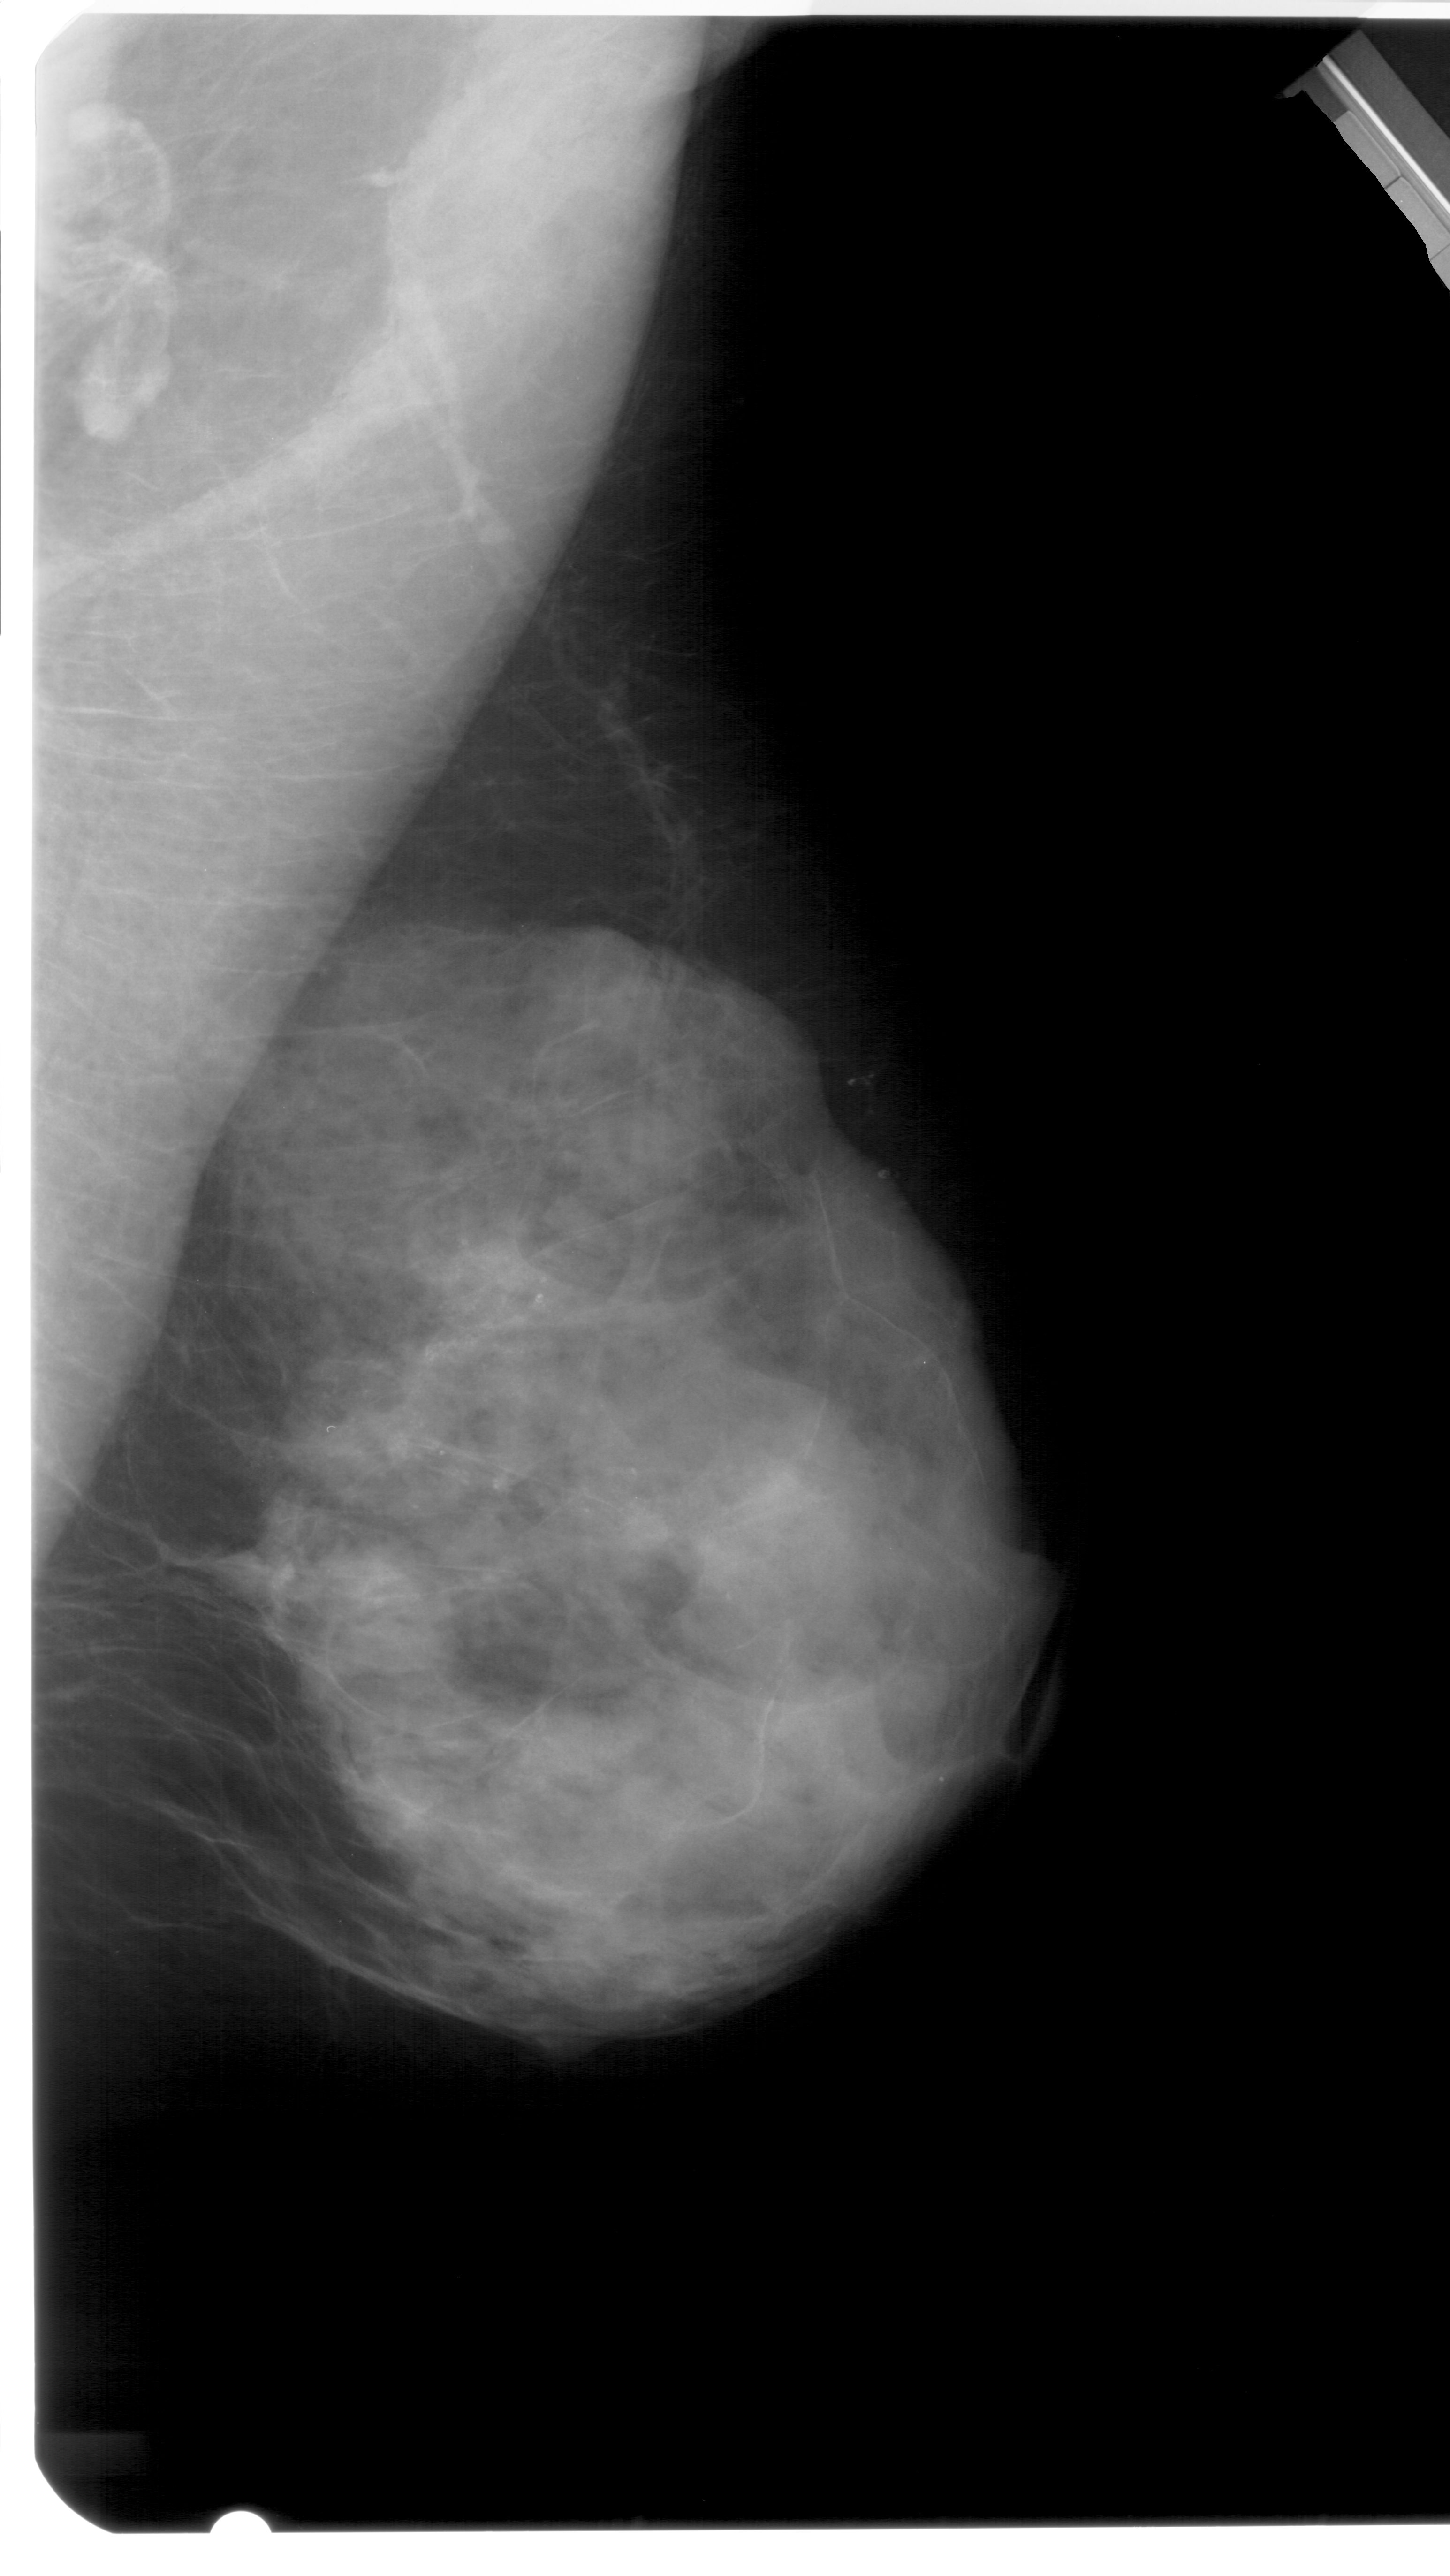
Digitized screen-film mammogram; right breast; MLO view; breast composition: extremely dense (BI-RADS density category 4 of 4); 1450 × 2576 image matrix.
Expert-marked regions of interest on this image (one box per marked abnormality):
- calcifications, morphology pleomorphic, distribution segmental; BI-RADS assessment category 4; subtlety rating 3 on a 1 (subtle) to 5 (obvious) scale; pathology (as recorded): benign: bounding box [x1, y1, x2, y2] px = [264, 1229, 660, 1560]